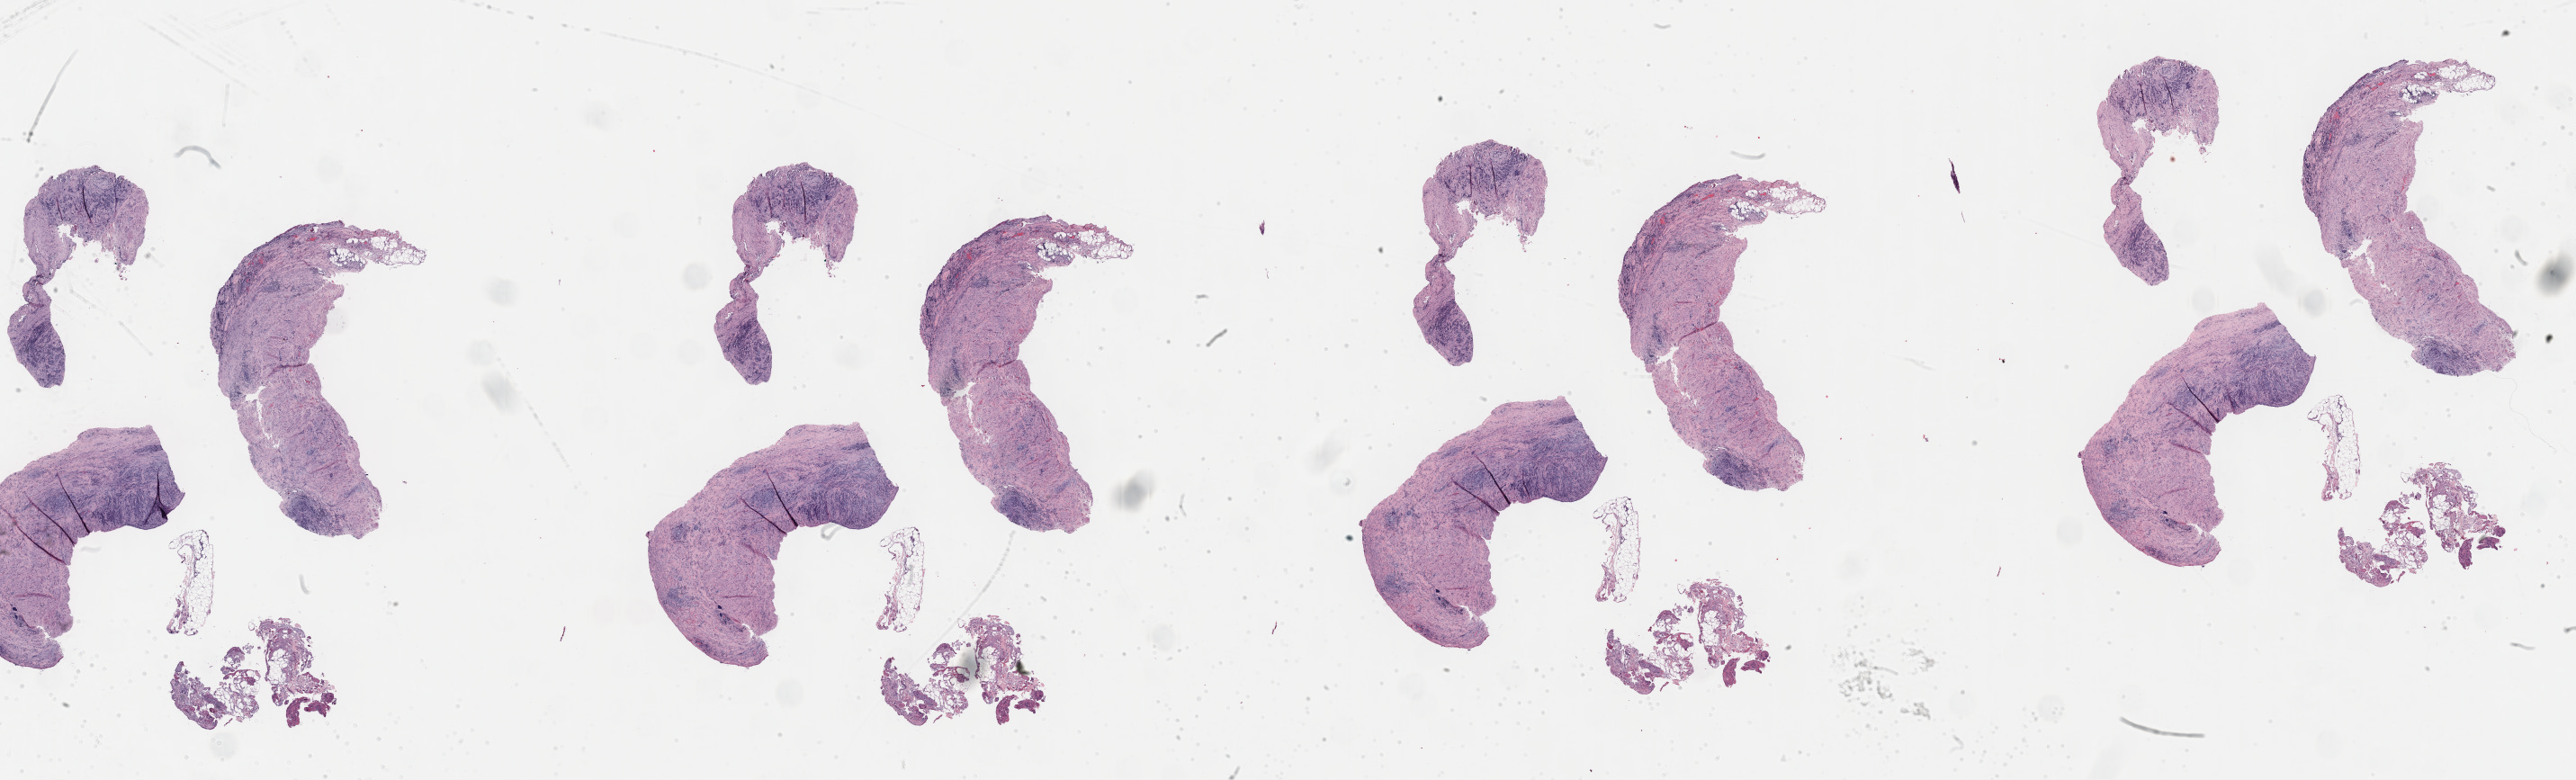
Digitized H&E-stained tissue section (whole slide) — whole scanned area (about 46.3 x 14.0 mm, from a 40x scan) shown as a low-resolution overview. FFPE section. Sample: primary tumour, pancreas. Patient: female, age at initial diagnosis 48 years. Histologic grade: G3 (poorly differentiated).
AJCC pathologic stage: IIB (7th edition). Diagnosis: Infiltrating duct carcinoma, NOS (head of pancreas).